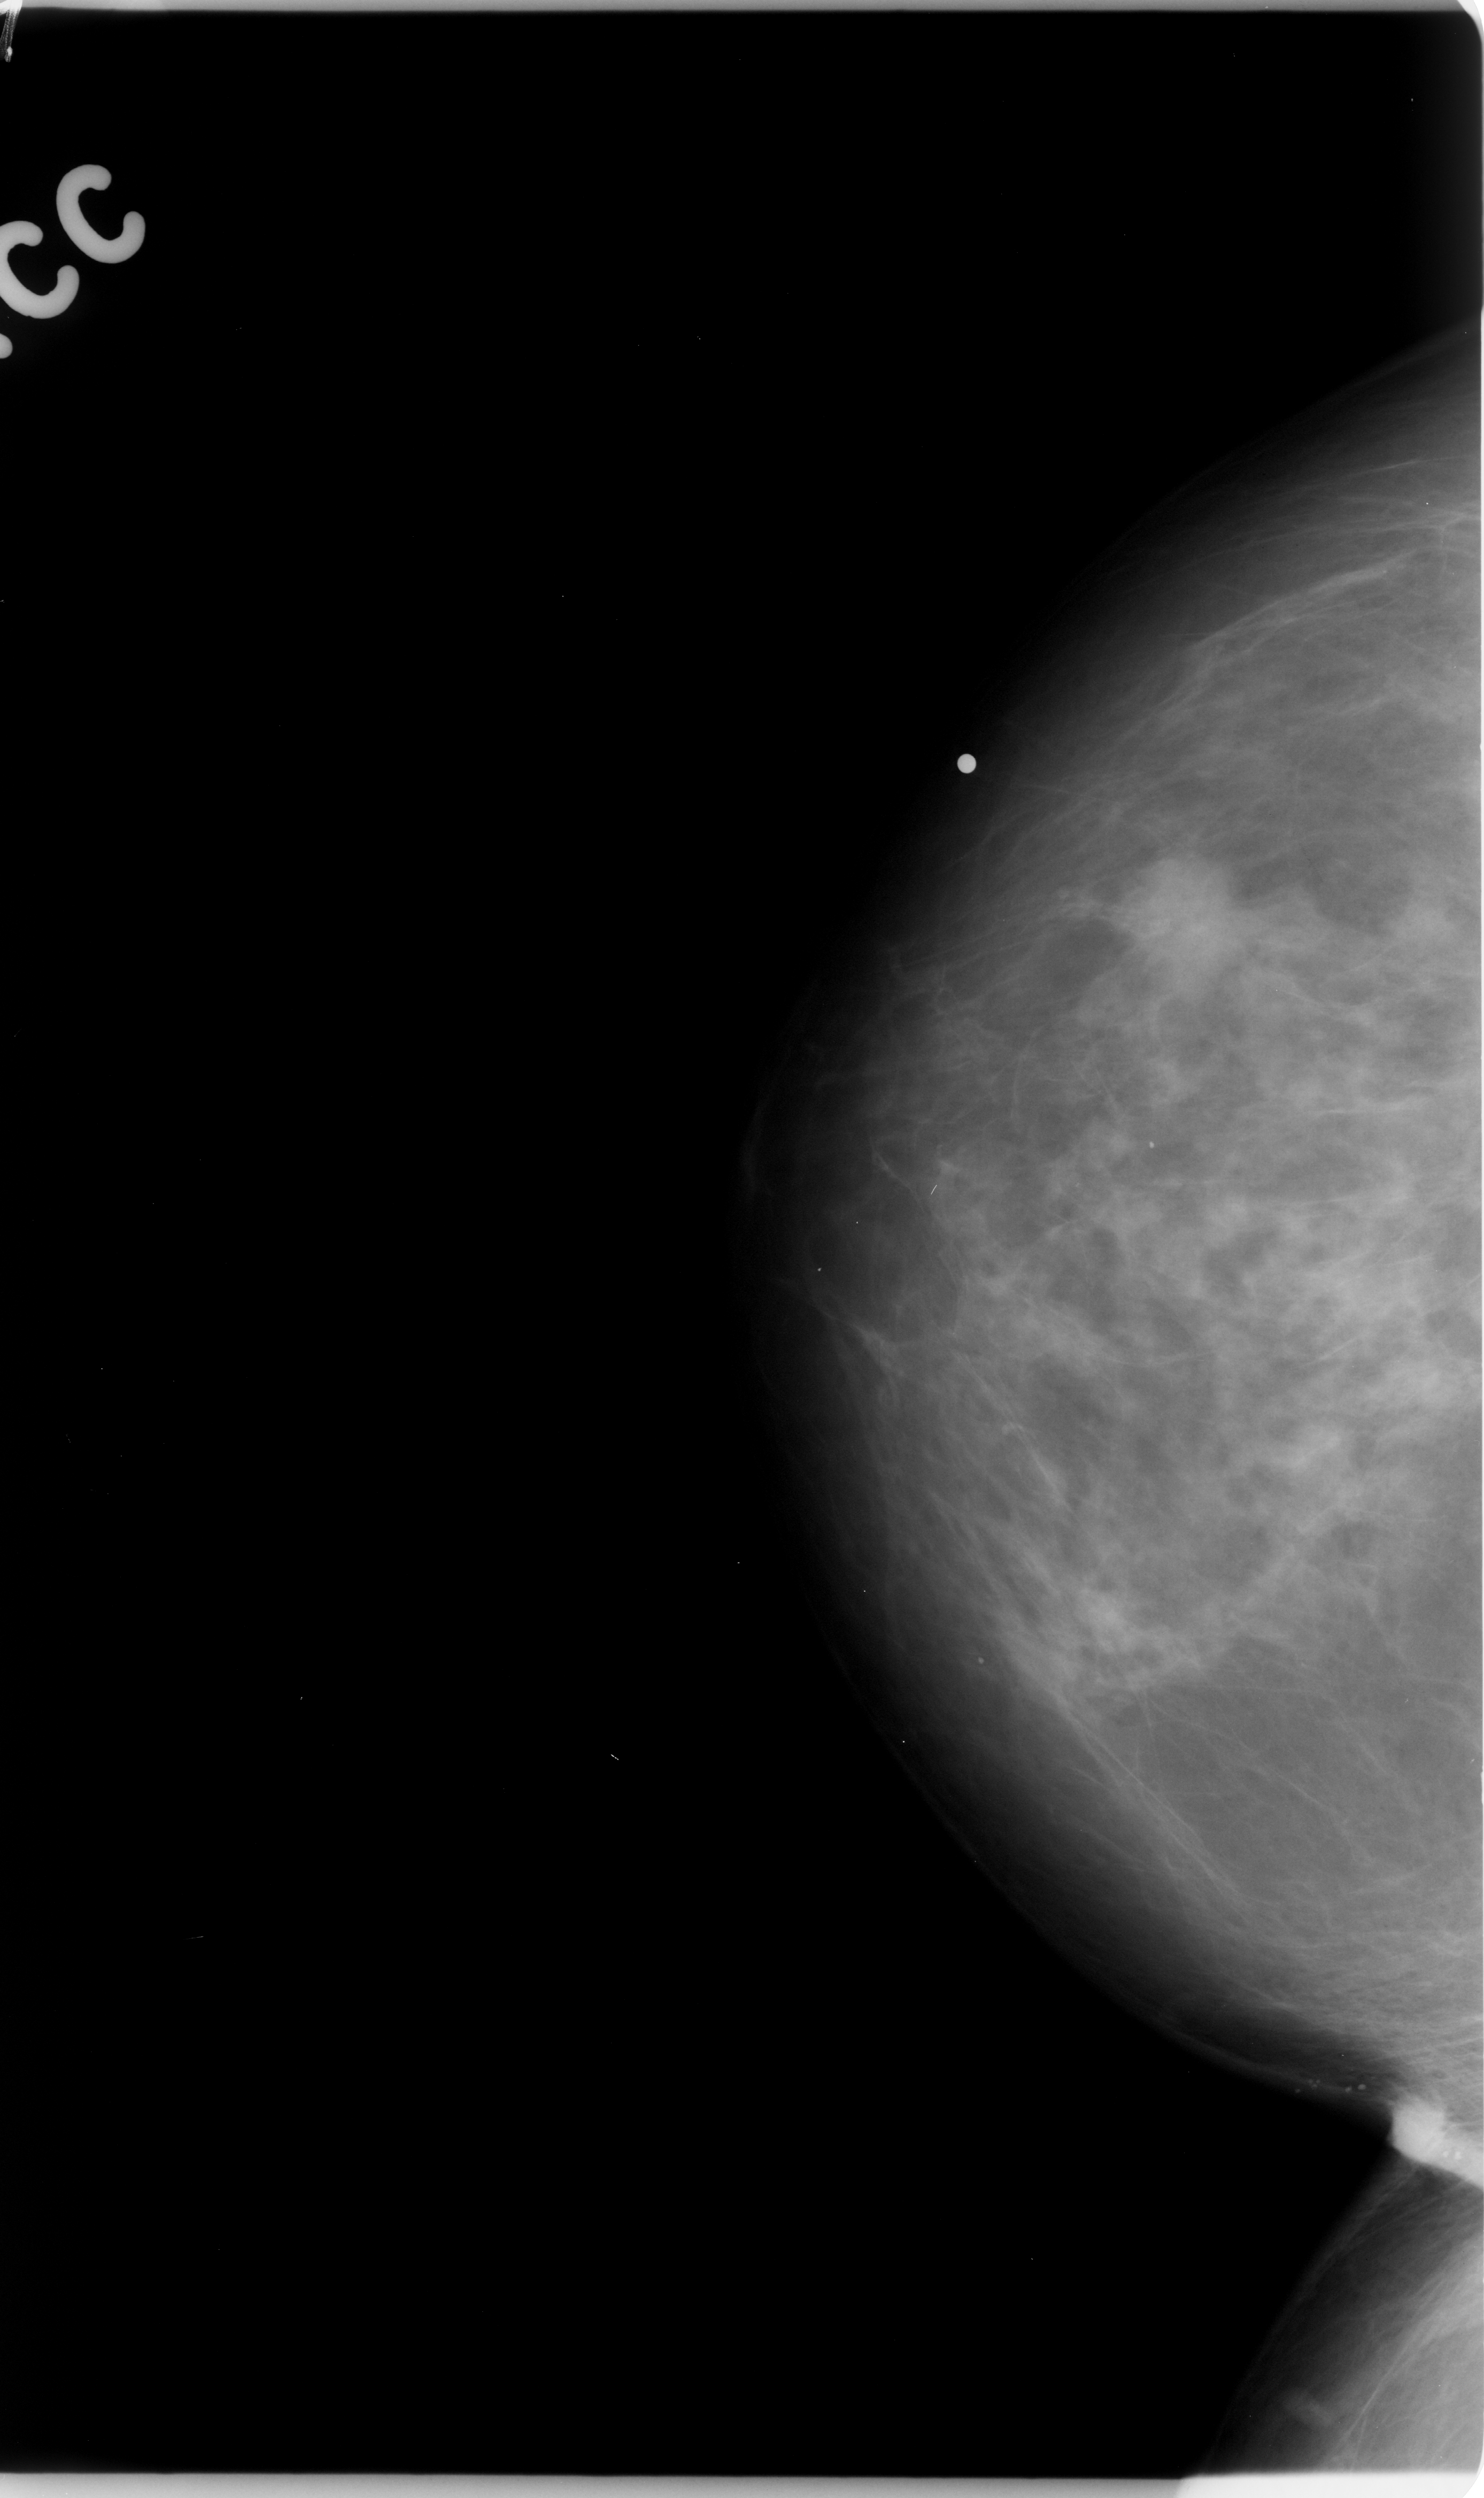
Mammogram (digitized film). Right breast. CC view. BI-RADS breast density category 2 (scale 1–4). 1484 × 2498 image matrix.
Expert-marked regions of interest on this film, with their recorded descriptors:
- mass, shape irregular, margins microlobulated; BI-RADS assessment category 5; pathology result (as recorded, not read from the image): malignant: box from (x=1096, y=850) to (x=1262, y=1001) px